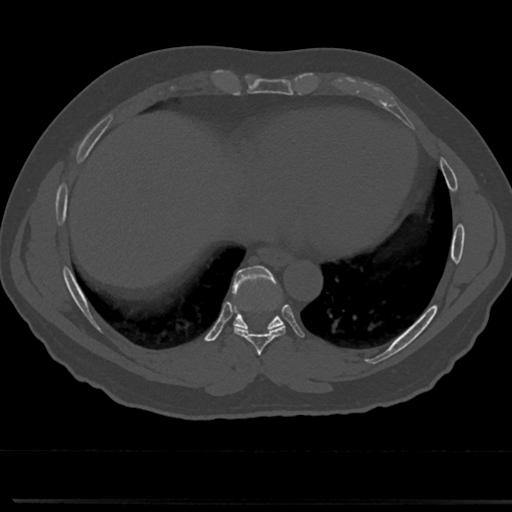
CT including the spine, one axial slice; position 336 of 817 along the scan axis; reconstruction kernel Br40s/3; 120 kVp; bone window (W 1800 / L 400 HU); 512 × 512 image matrix, field of view 355 × 355 mm. Patient: male, 61 years. Case-level facts recorded for this patient, not image findings: primary cancer: prostate.
Annotated regions visible in this slice (semi-automatically segmented with operator editing):
- T7 vertebra: bounding box <258,345,266,377> (left, top, right, bottom; pixels)
- T8 vertebra: <212,271,309,355>